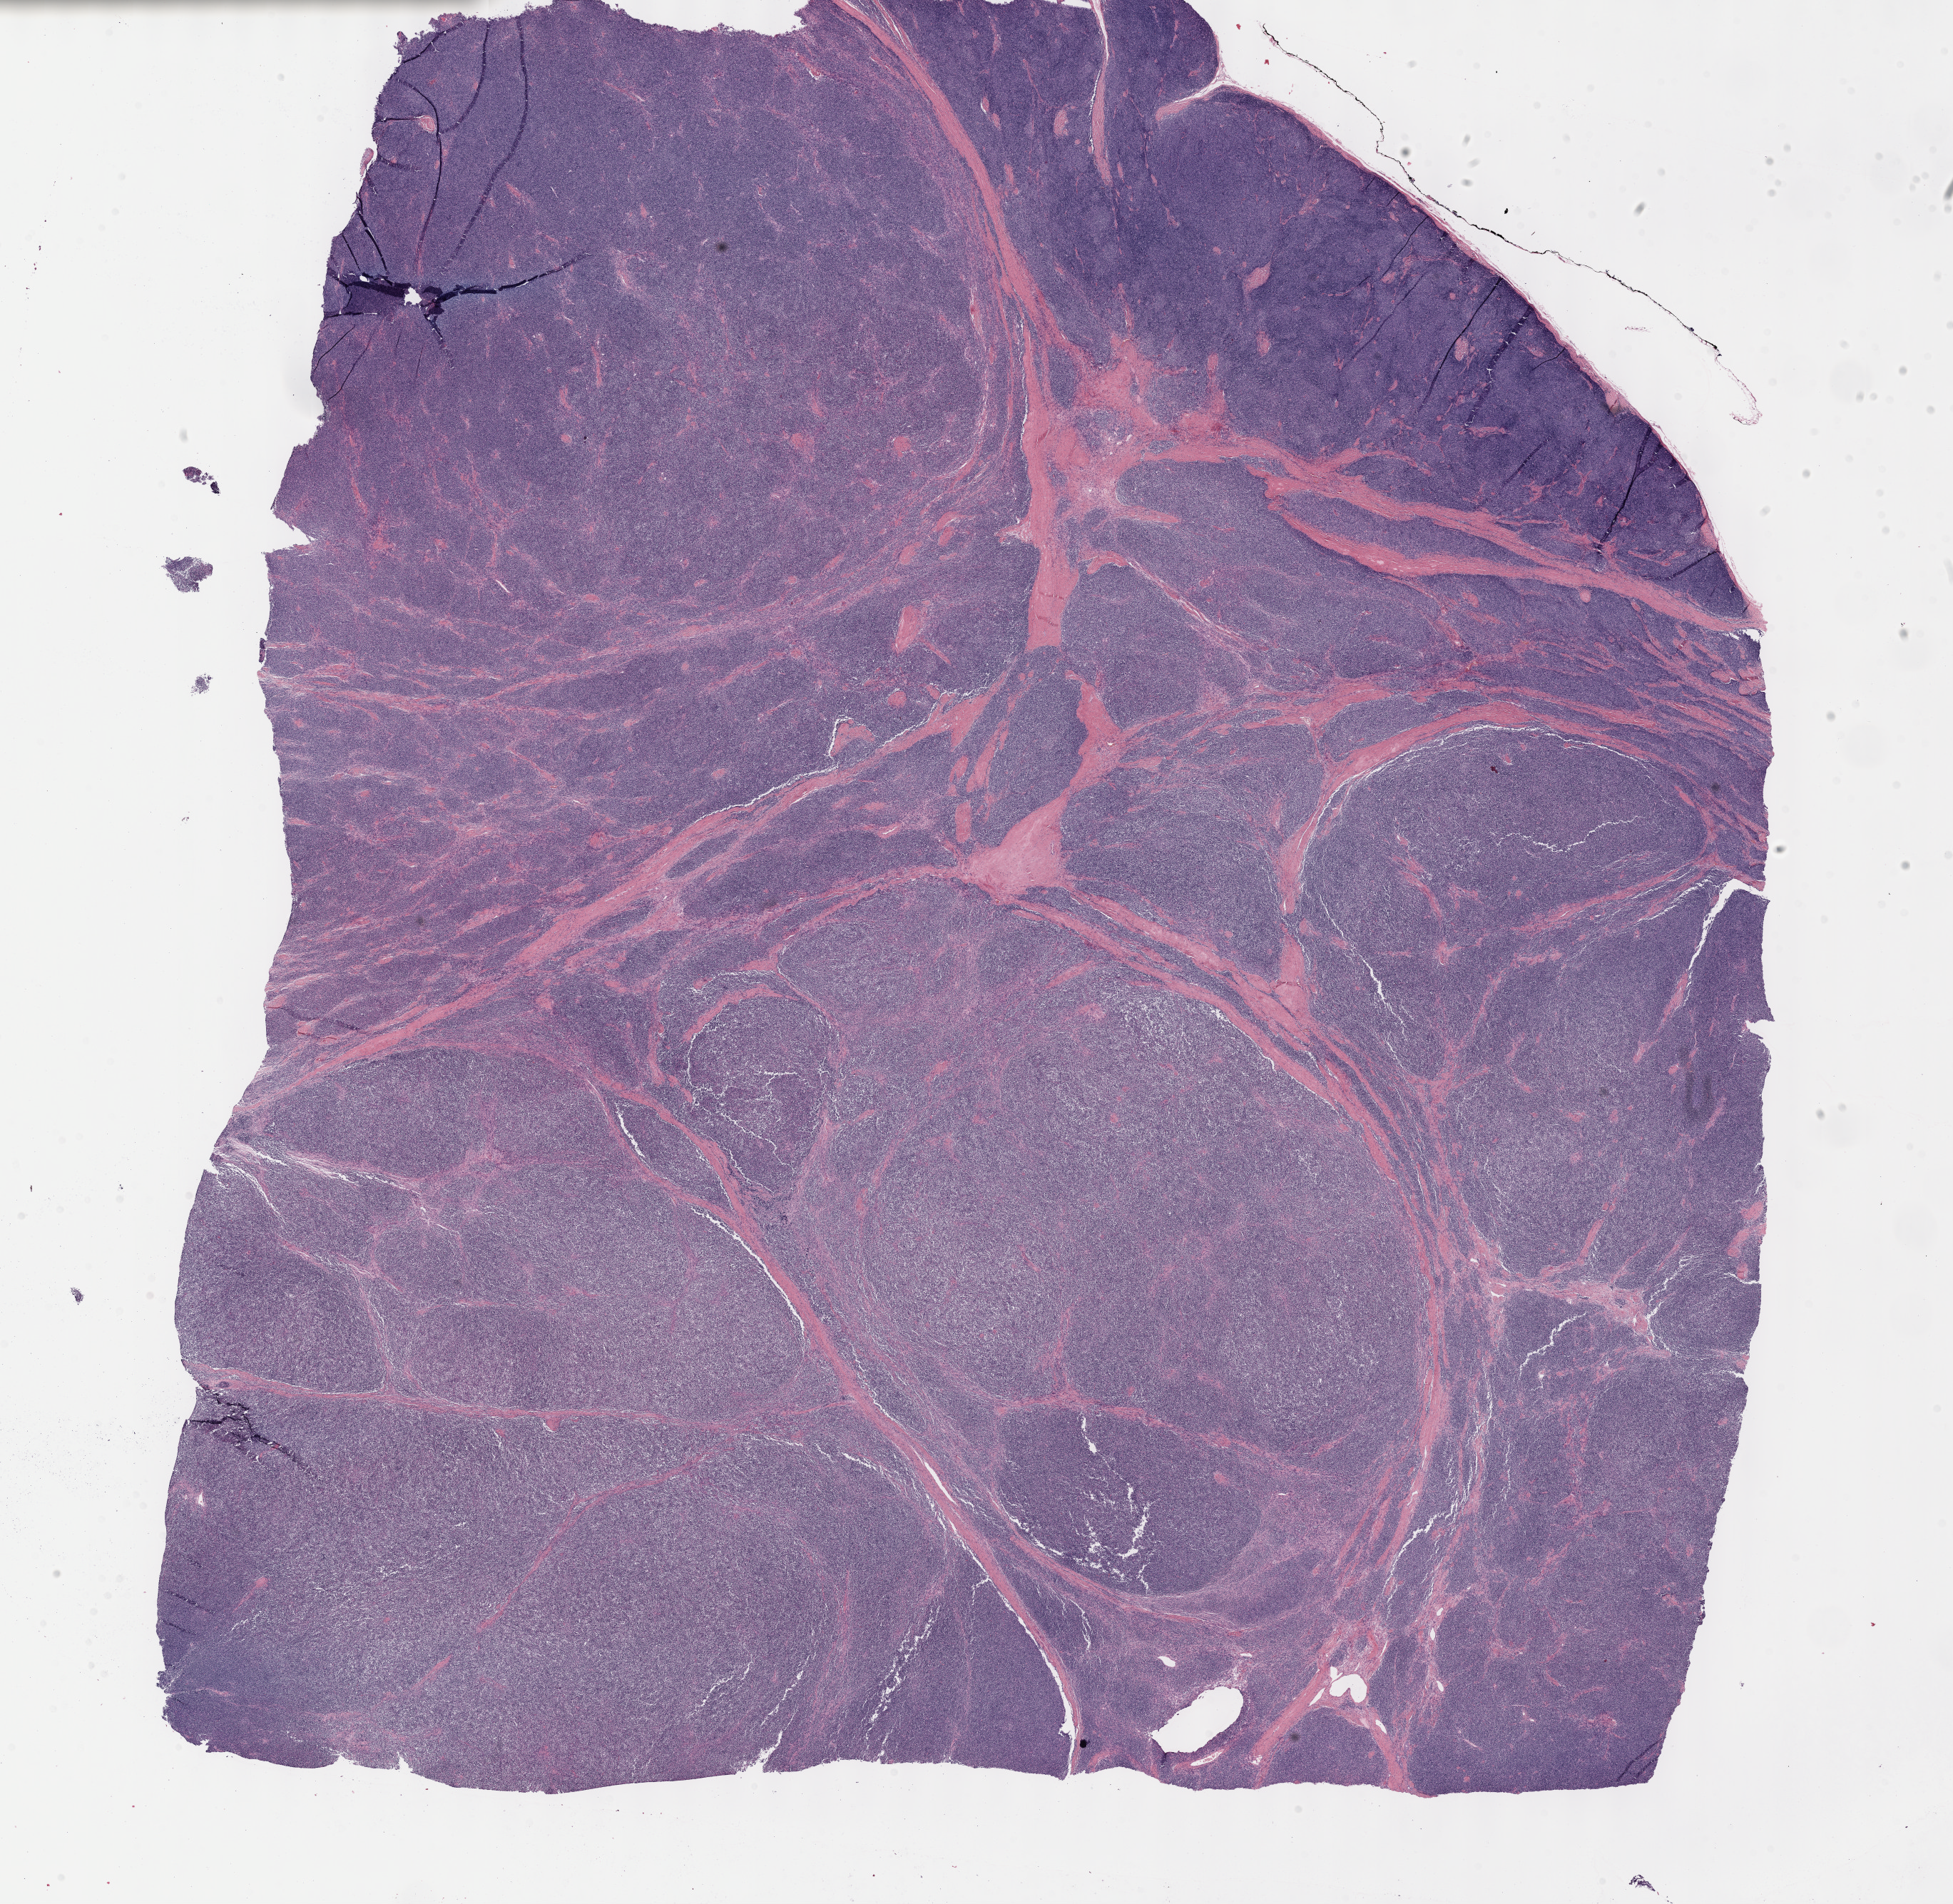
Whole-slide histology image, Hematoxylin and eosin (H&E) stained — shown as a low-resolution overview of the whole scanned area (about 22.1 x 21.6 mm, from a 40x scan), FFPE section, thymus, primary tumour sample. Male, age 52 years at initial diagnosis.
Histologic diagnosis: Thymoma, type B2, NOS.